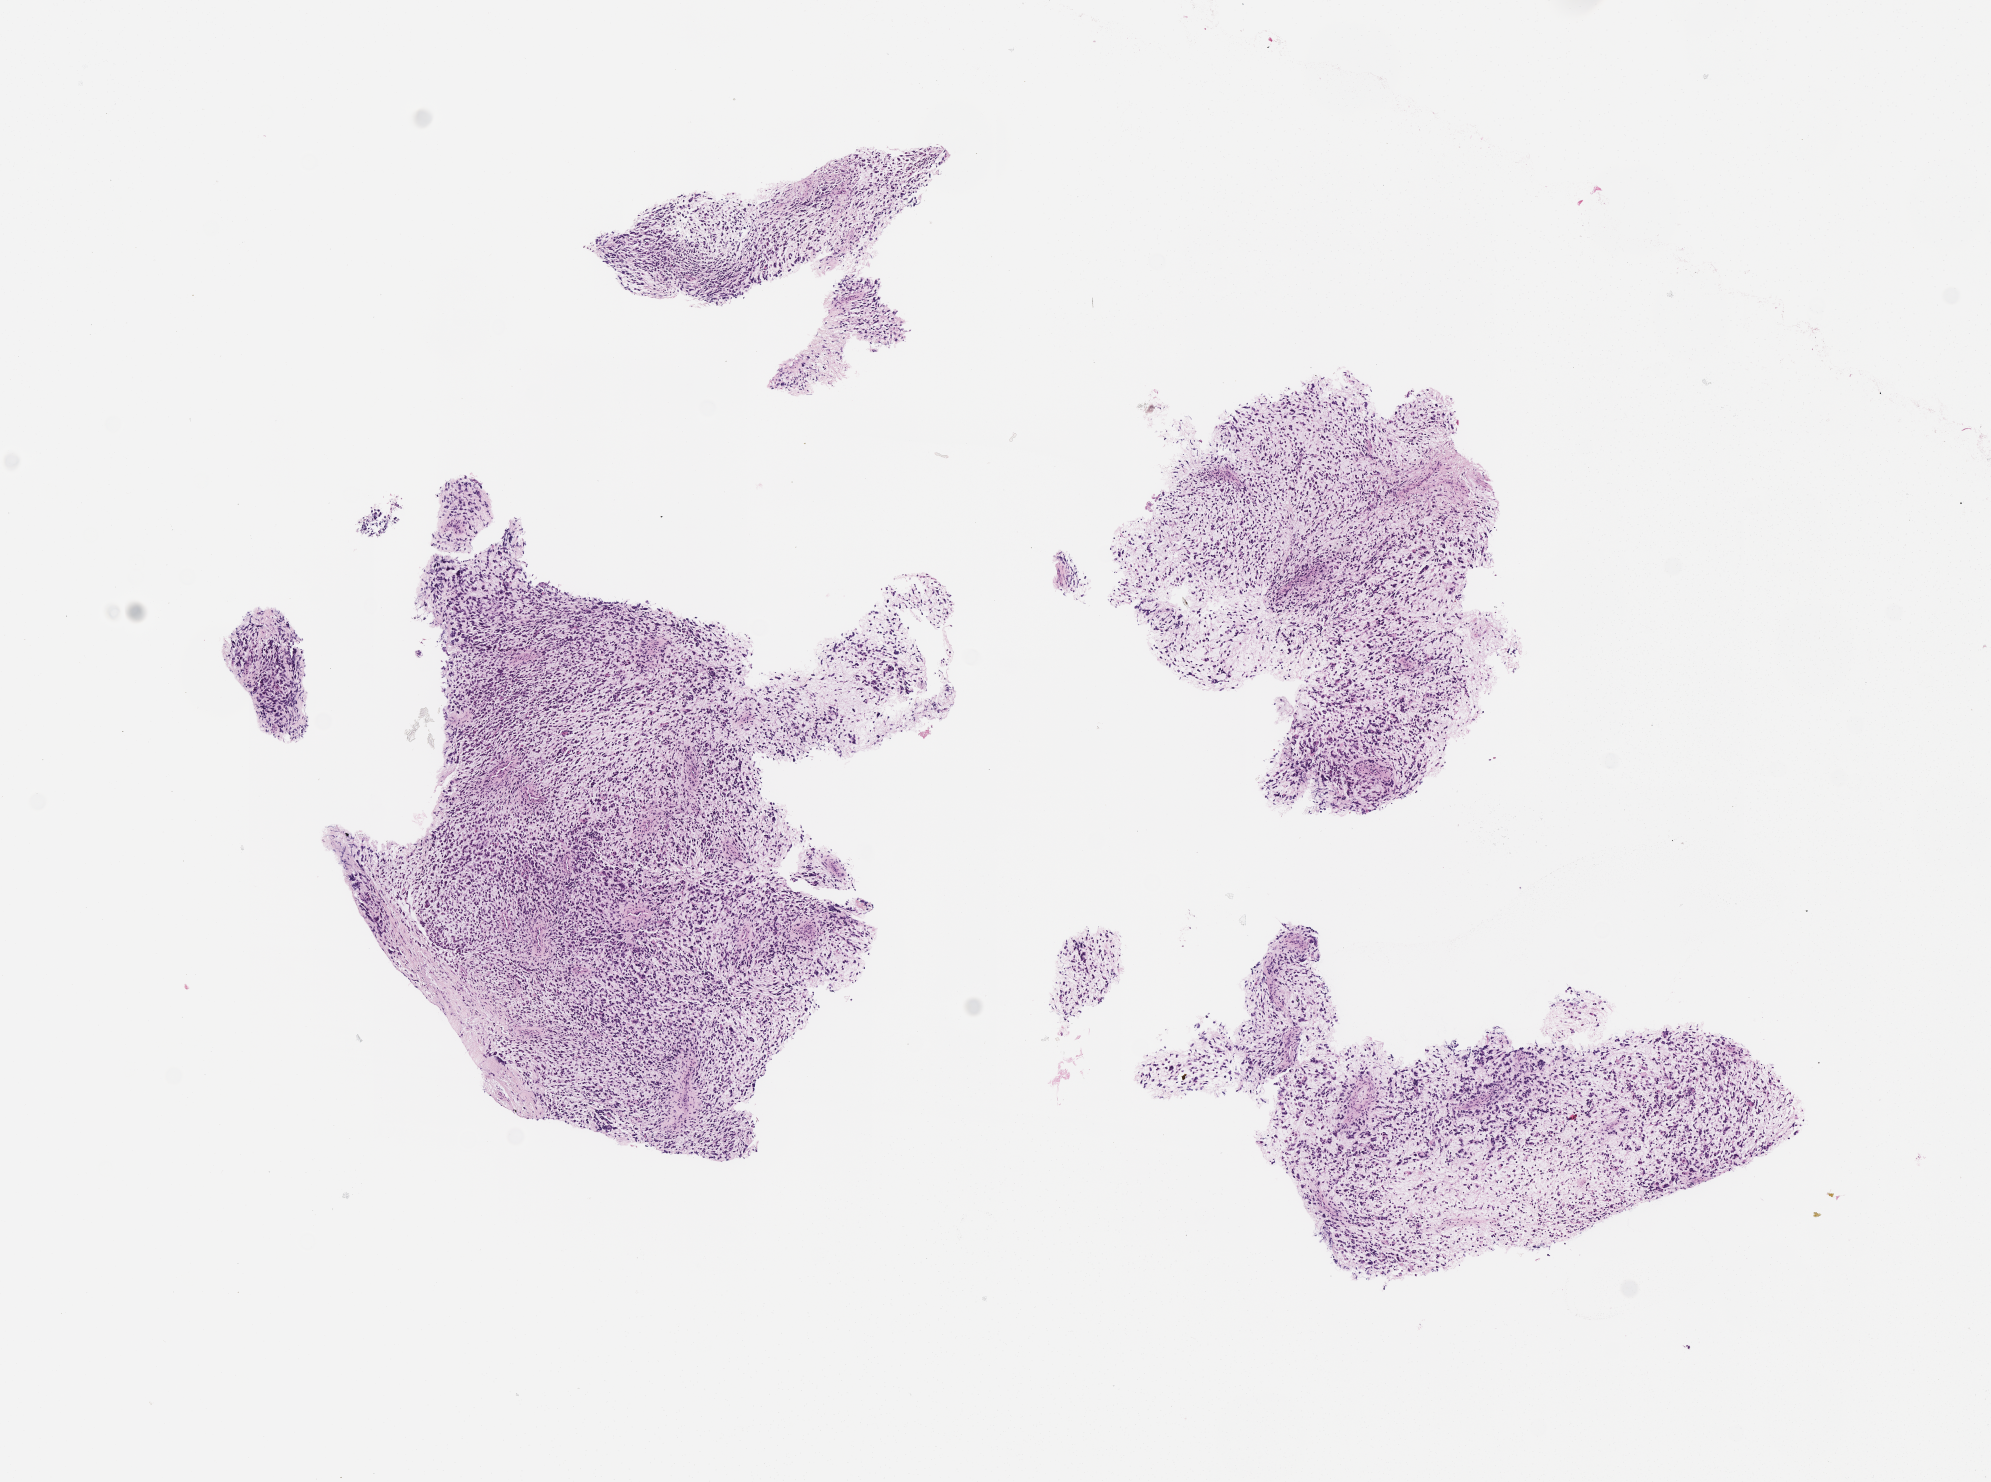
Digitized haematoxylin and eosin-stained section of tumor tissue — a low-resolution overview of the entire scanned area, about 8.1 x 6.0 mm; FFPE section; sample anatomic site: paratesticular, right. Male patient, age at diagnosis 8.1 years.
Stage (as recorded): 1. Diagnosis: rhabdomyosarcoma; histological classification: embryonal rhabdomyosarcoma. Metastatic status at presentation (as recorded): non-metastatic. Primary site (case record): testis-Paratestis.